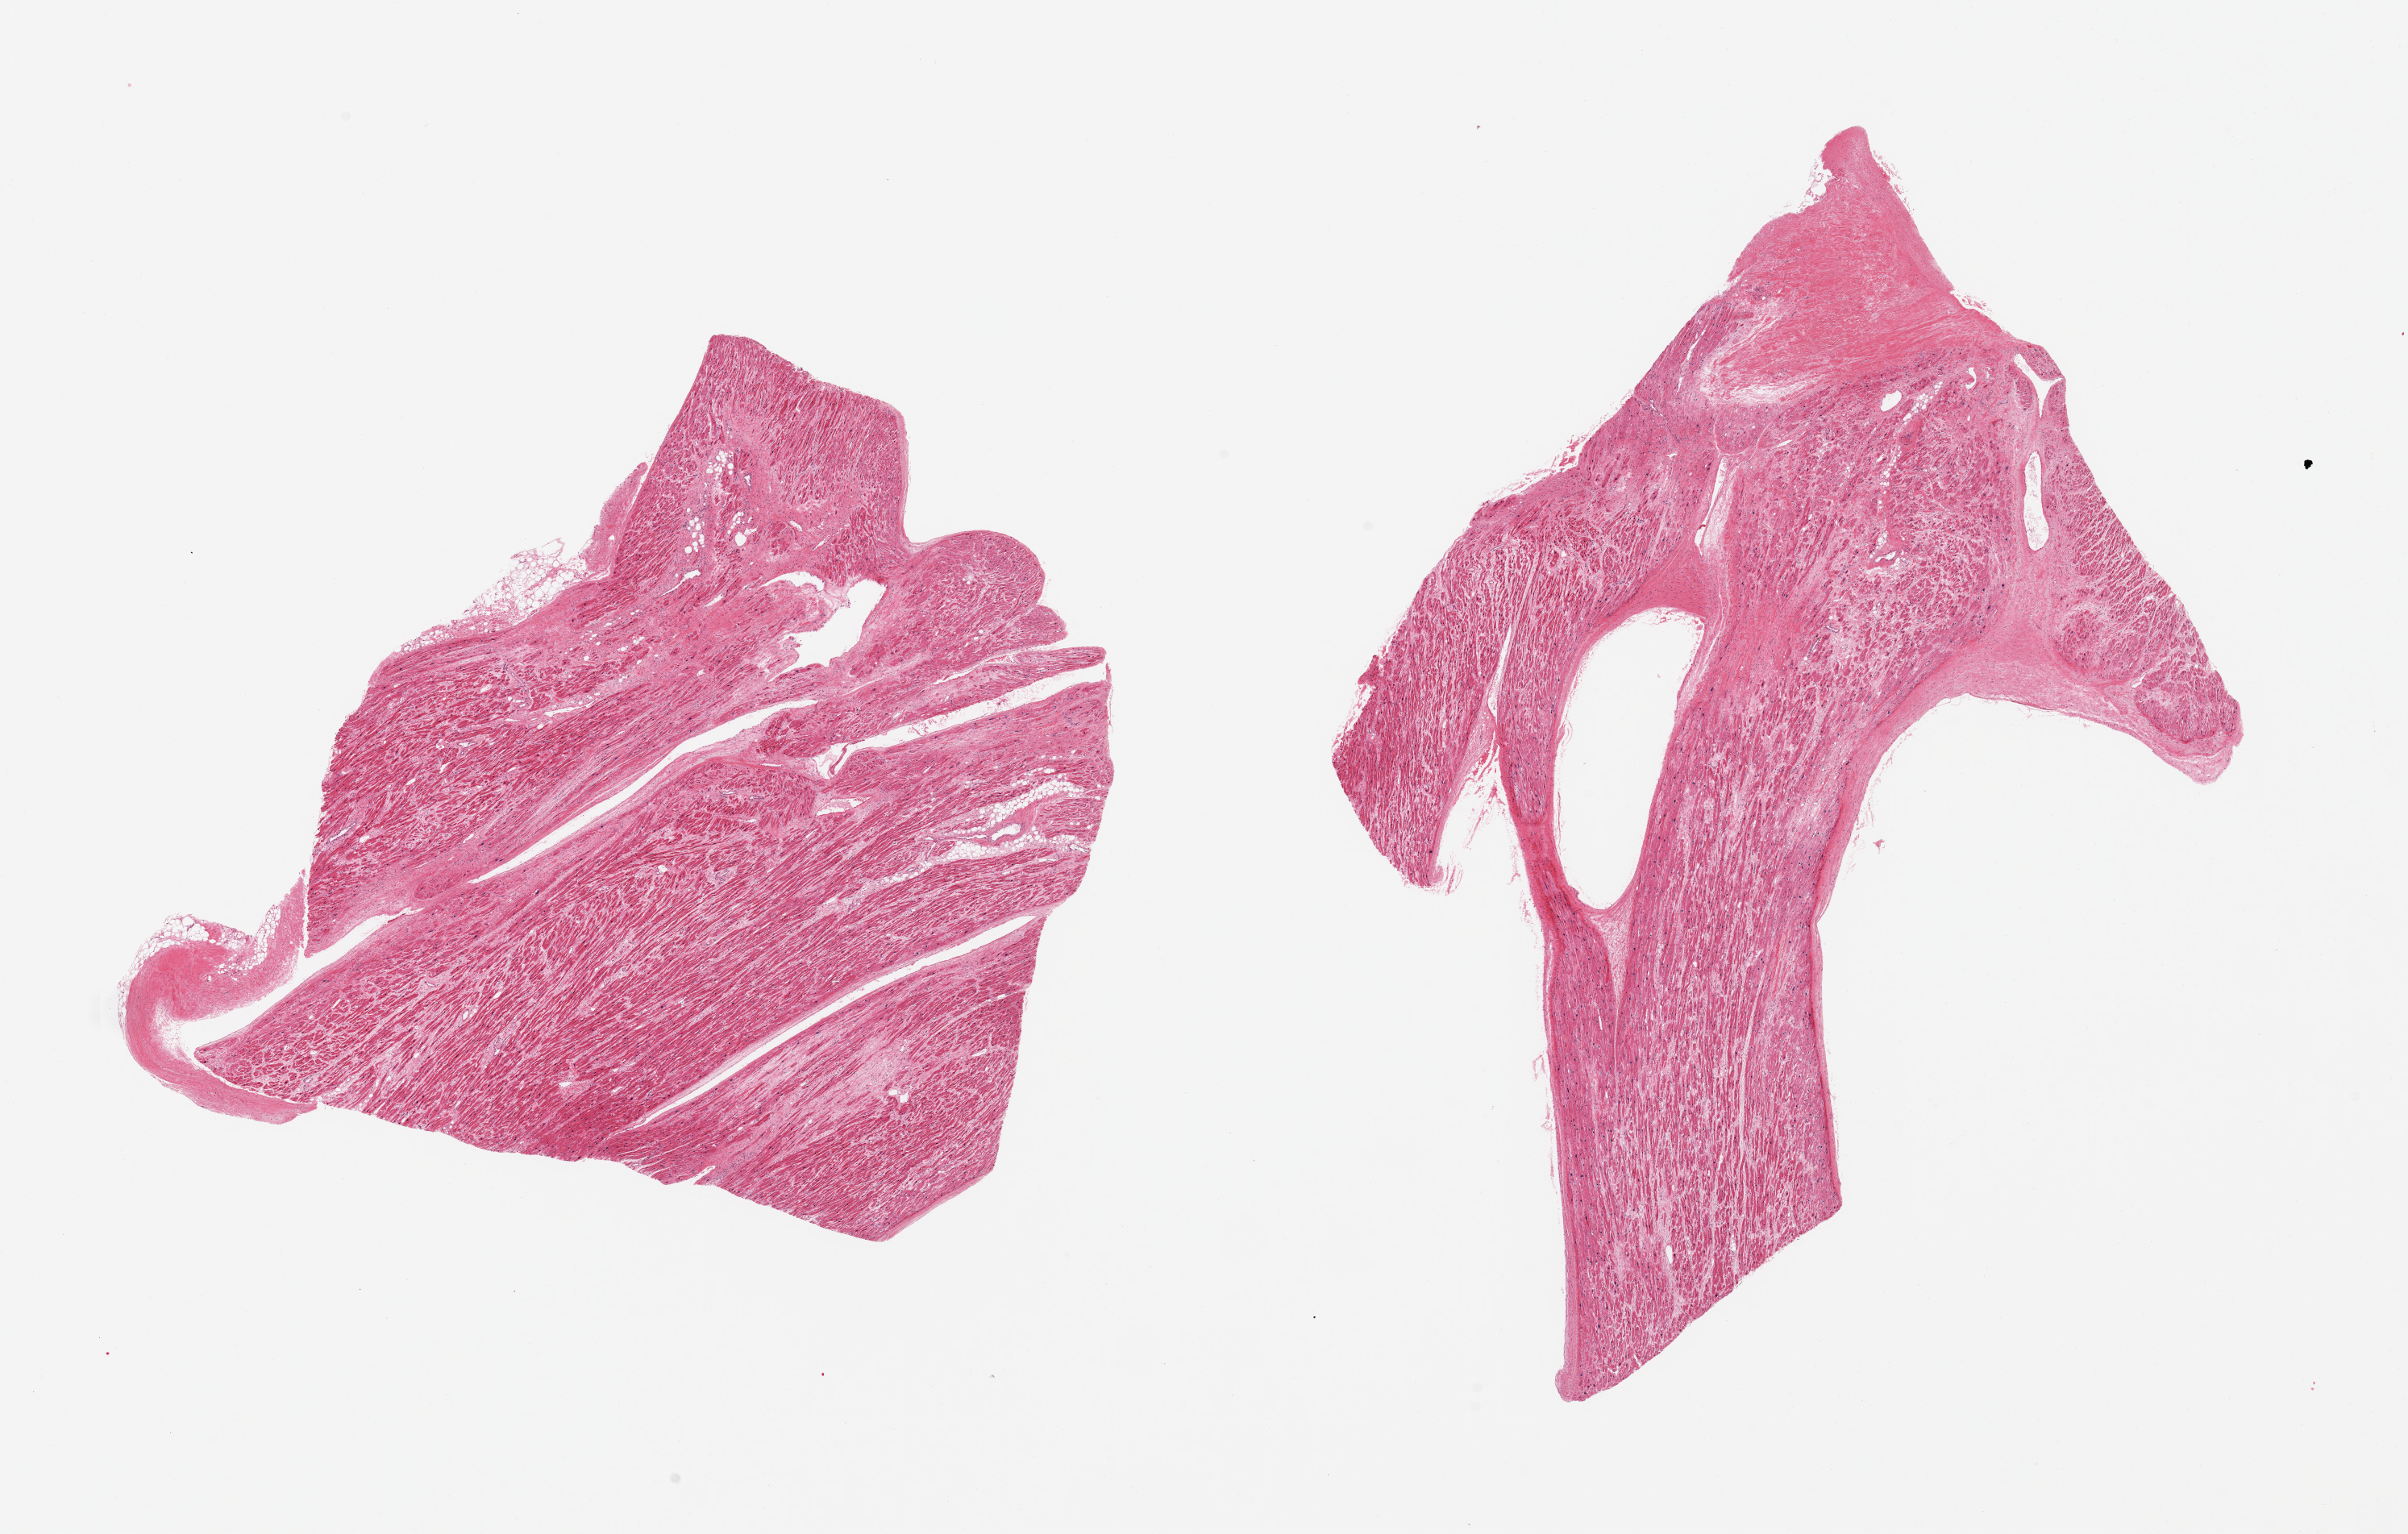
Hematoxylin and eosin (H&E) whole-slide image, shown as a low-resolution overview of the whole scanned area (about 23.6 x 15.1 mm, slide scanned at 20x); PAXgene-fixed, paraffin-embedded tissue; target tissue: auricular appendage; donor tissue sample. Donor: male.
* pathologist's review note for this sample: 2 pieces, no abnormalities